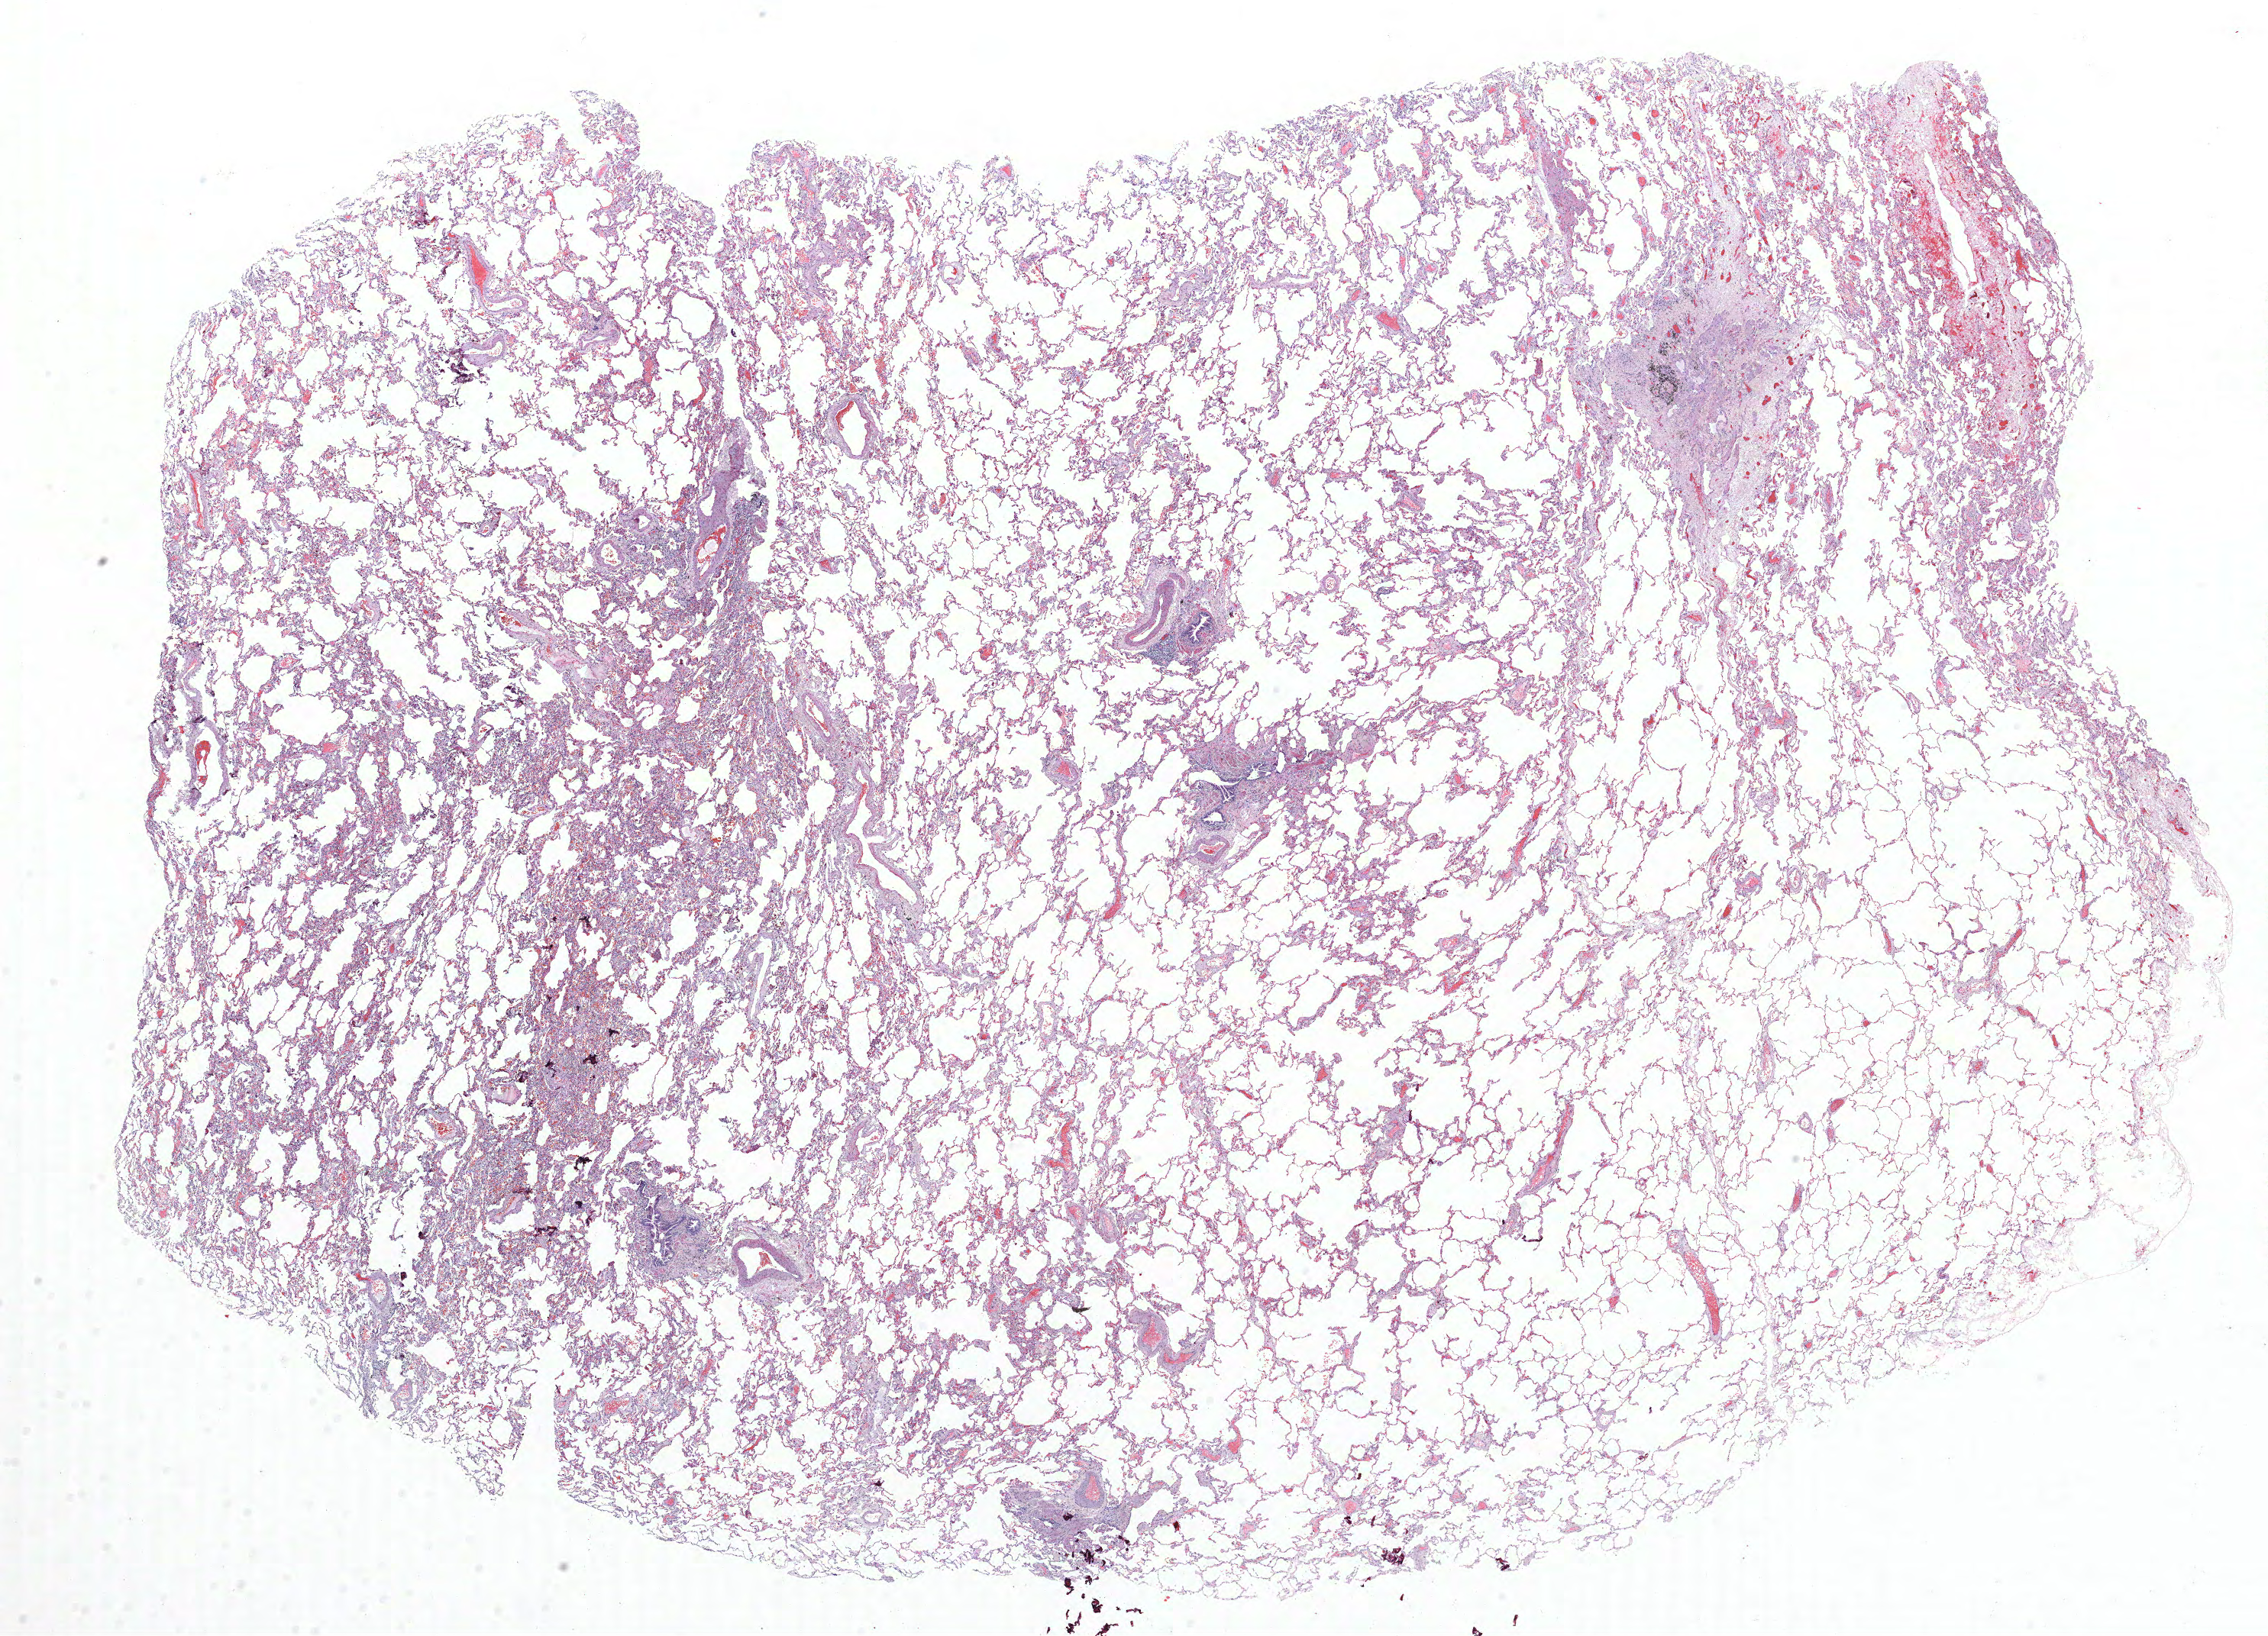
Whole-slide histology image, Hematoxylin and eosin (H&E) stained, a low-resolution overview of the entire scanned area, about 23.8 x 17.1 mm (acquisition: 40x scan), FFPE section, lung. Female patient, aged 57 at enrolment. Current smoker at enrolment. Grade: well differentiated (G1).
Participant's lung-cancer diagnosis: Bronchiolo-alveolar adenocarcinoma, NOS (ICD-O-3 8250/3). Primary tumour location (clinical record): left lower lobe. ICD-O-3 topography: lower lobe of lung (C34.3). Tumour size (pathology): 16 mm. Stage (AJCC 6th edition): IA.